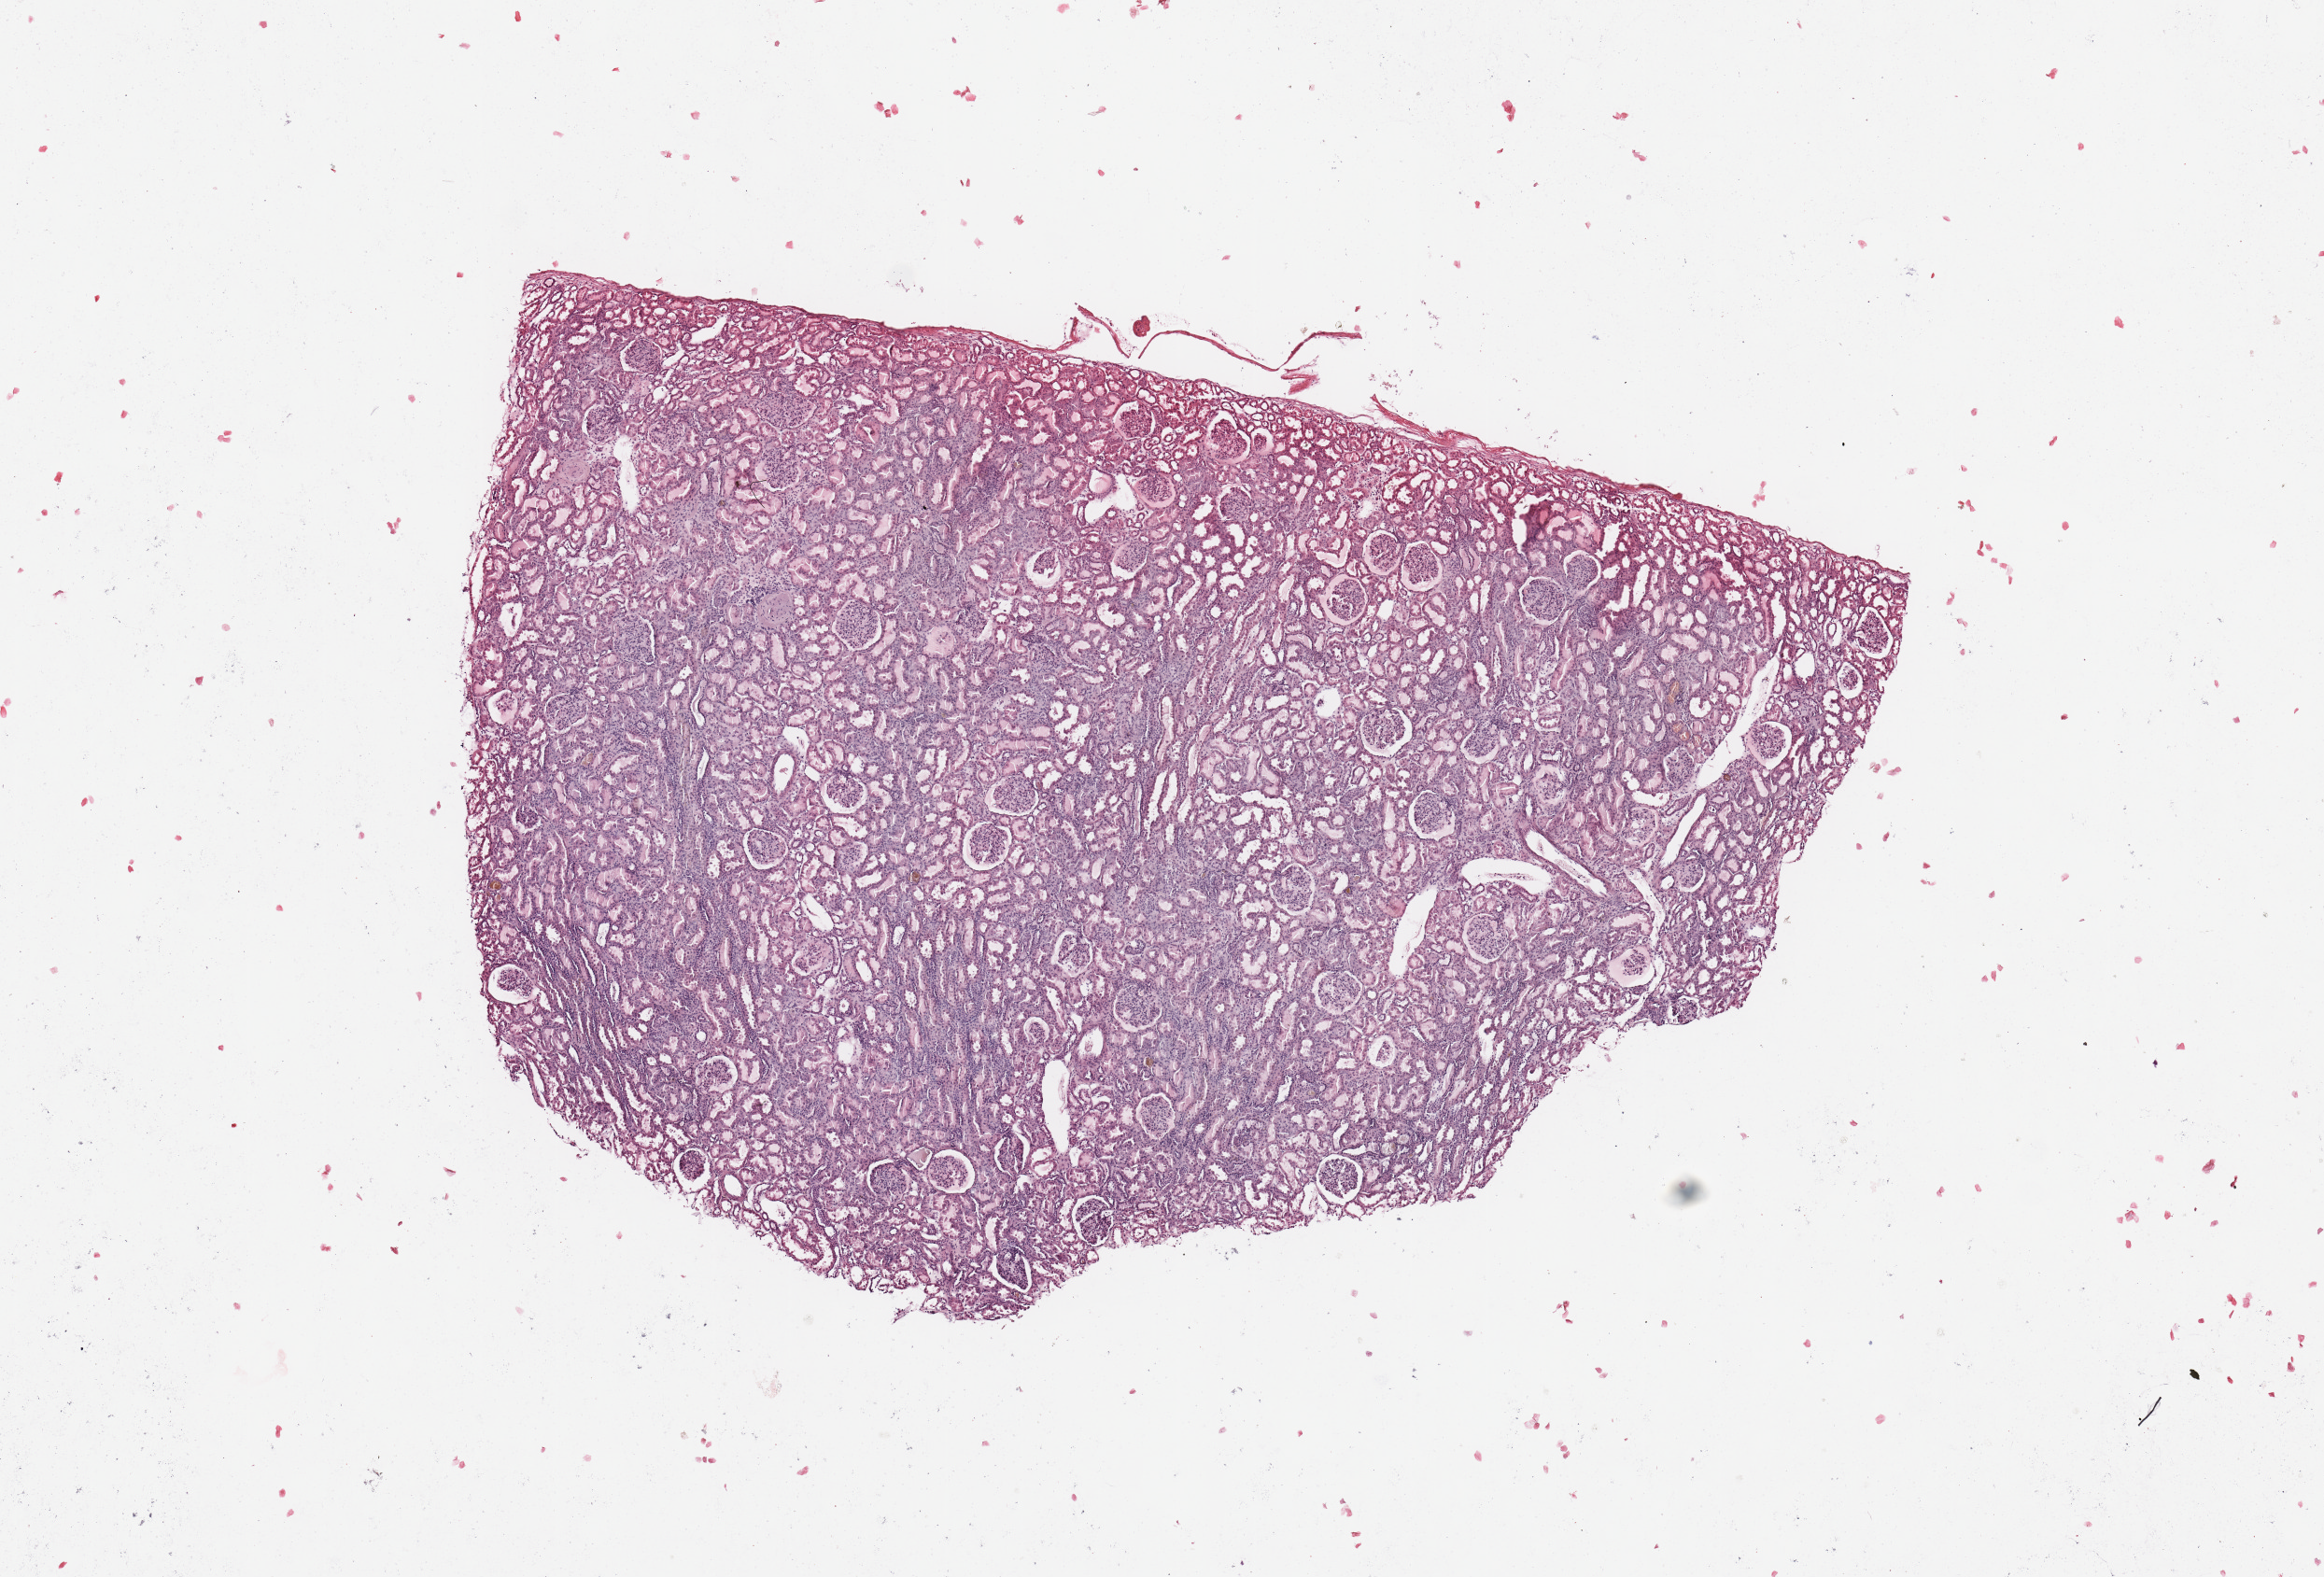
Digitized H&E tissue section (whole slide), whole scanned area (about 9.8 x 6.7 mm, acquisition: 20x scan) shown as a low-resolution overview. Normal (non-tumour) tissue sample, sampled site: kidney. 46-year-old male patient.
• this section: normal (non-tumour) tissue from the same patient
• patient diagnosis: Renal cell carcinoma, NOS